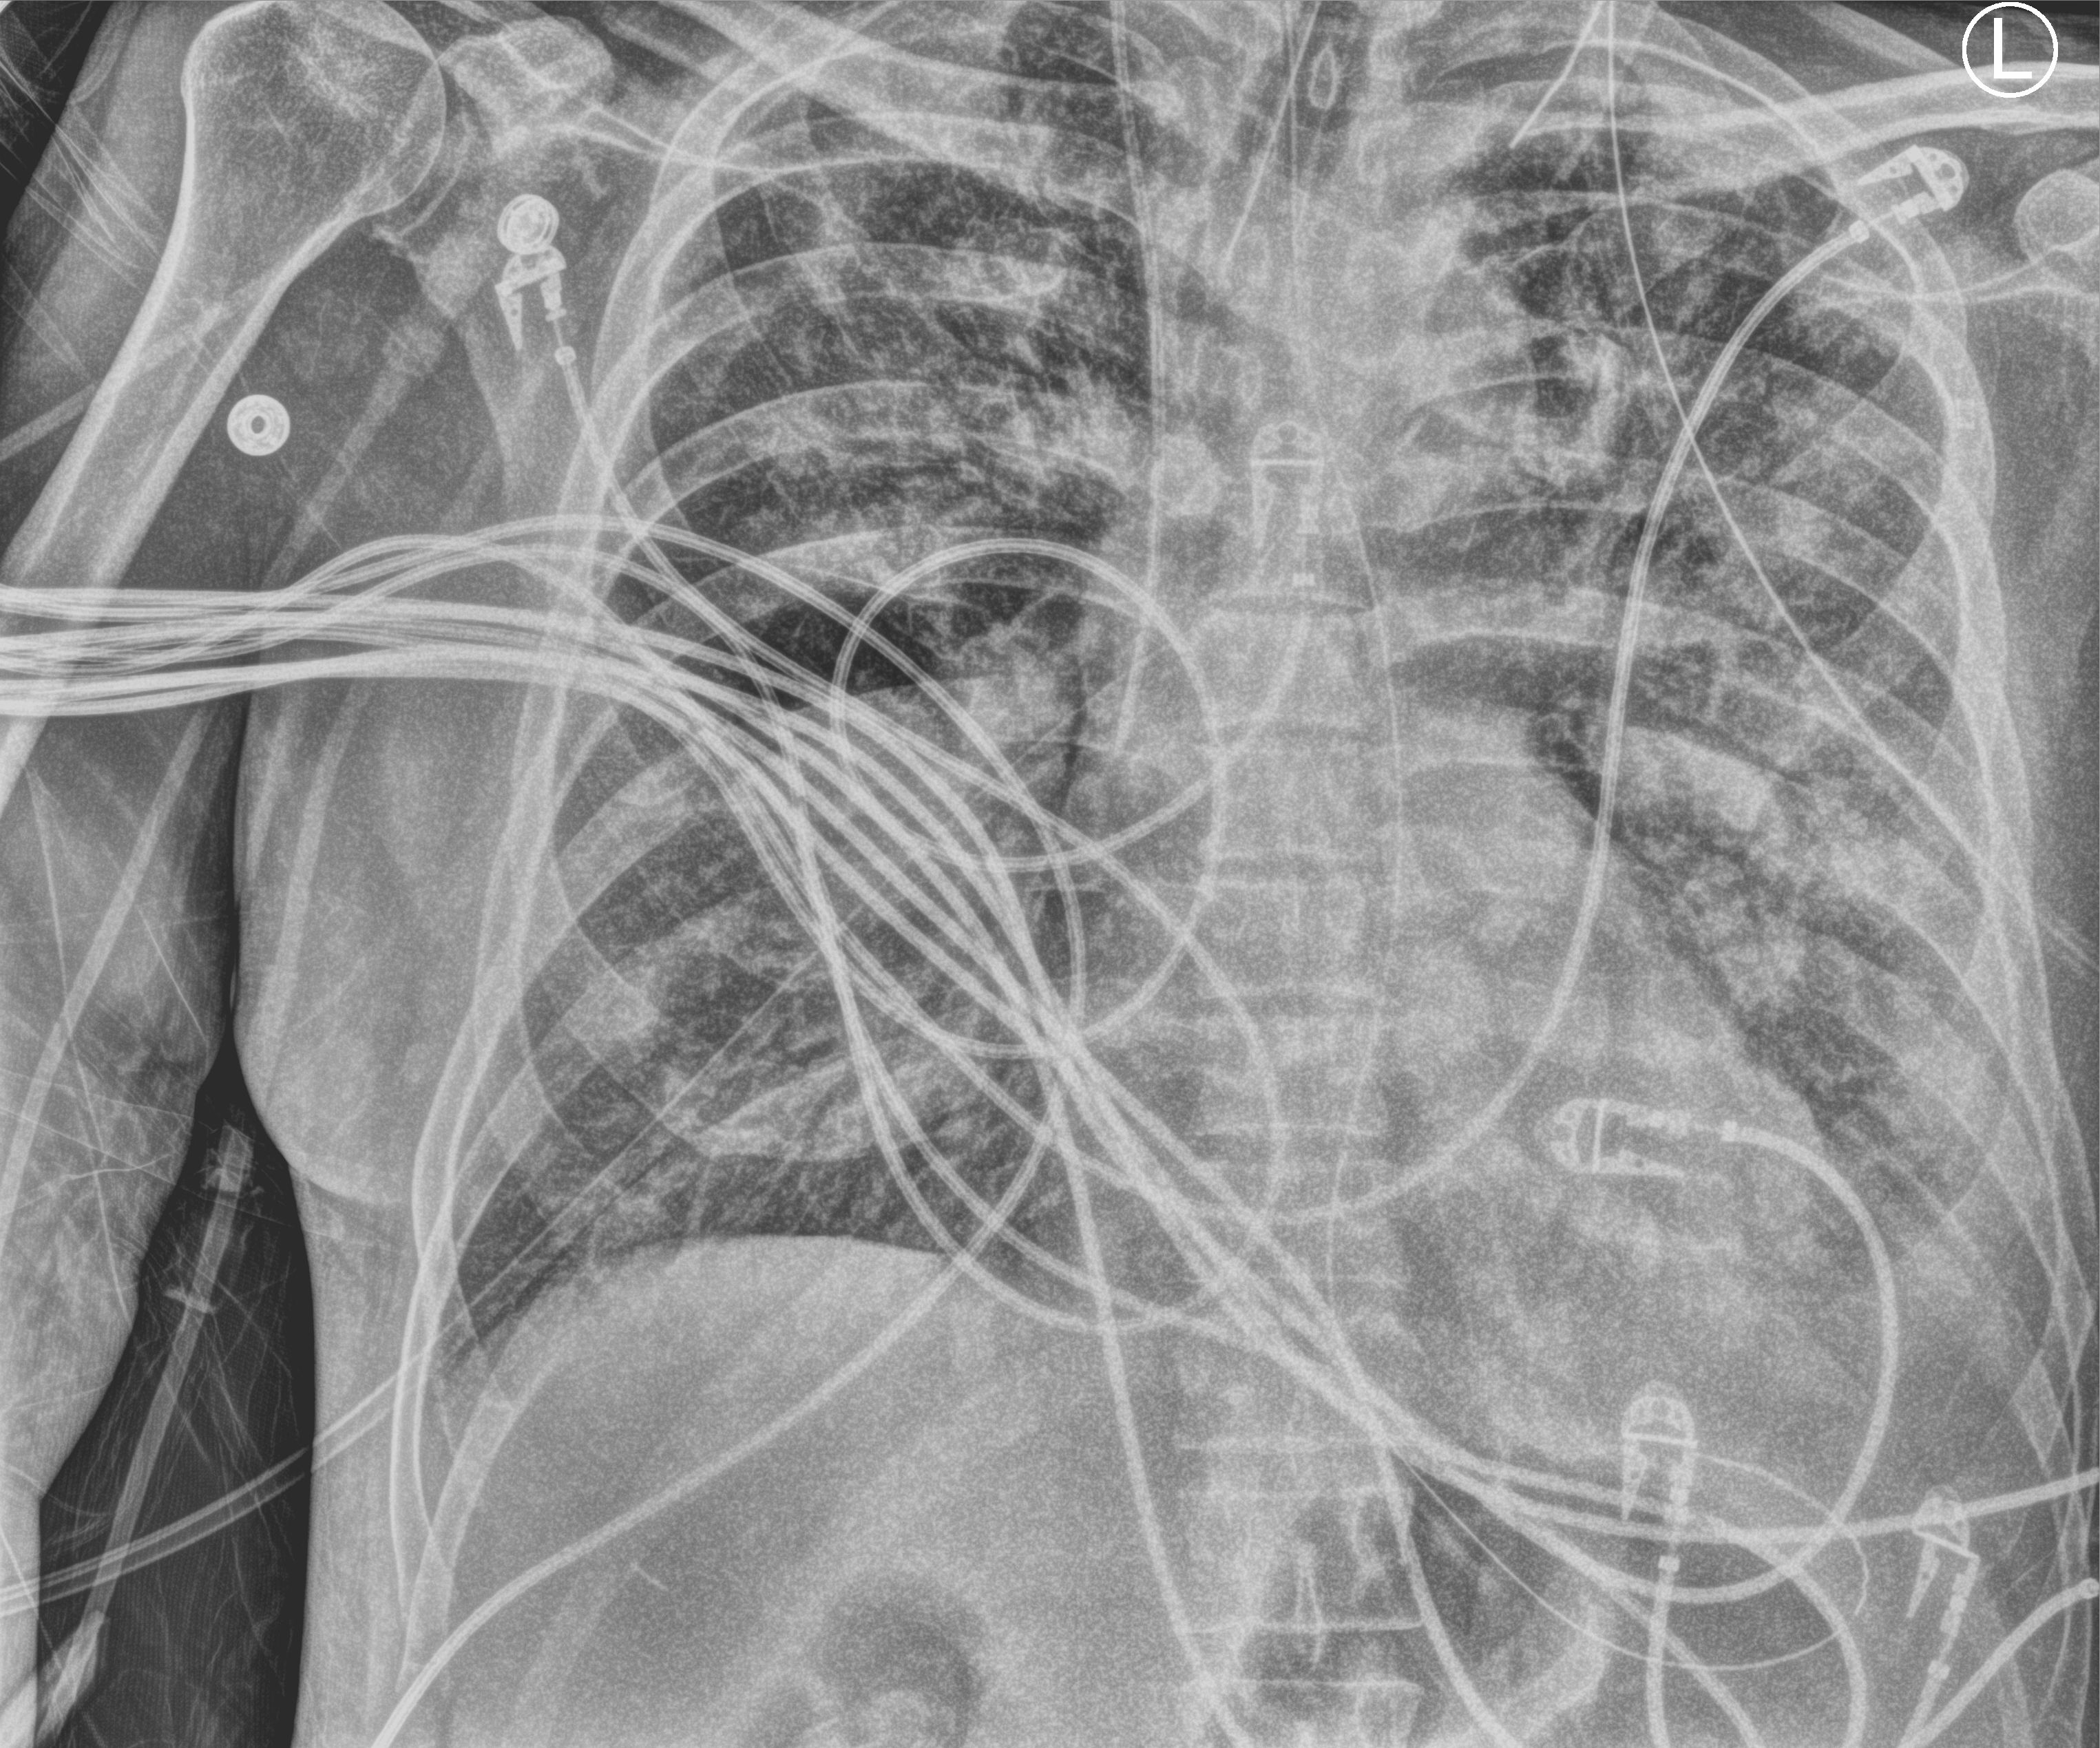
Portable chest radiograph, anteroposterior (AP) projection. Patient hospitalised with COVID-19; male, aged 60–74 years.
From the hospital-stay record, not from the radiograph (when in the stay this image was taken is not recorded): admitted to intensive care during this hospital stay: yes; mechanically ventilated during this hospital stay: yes.